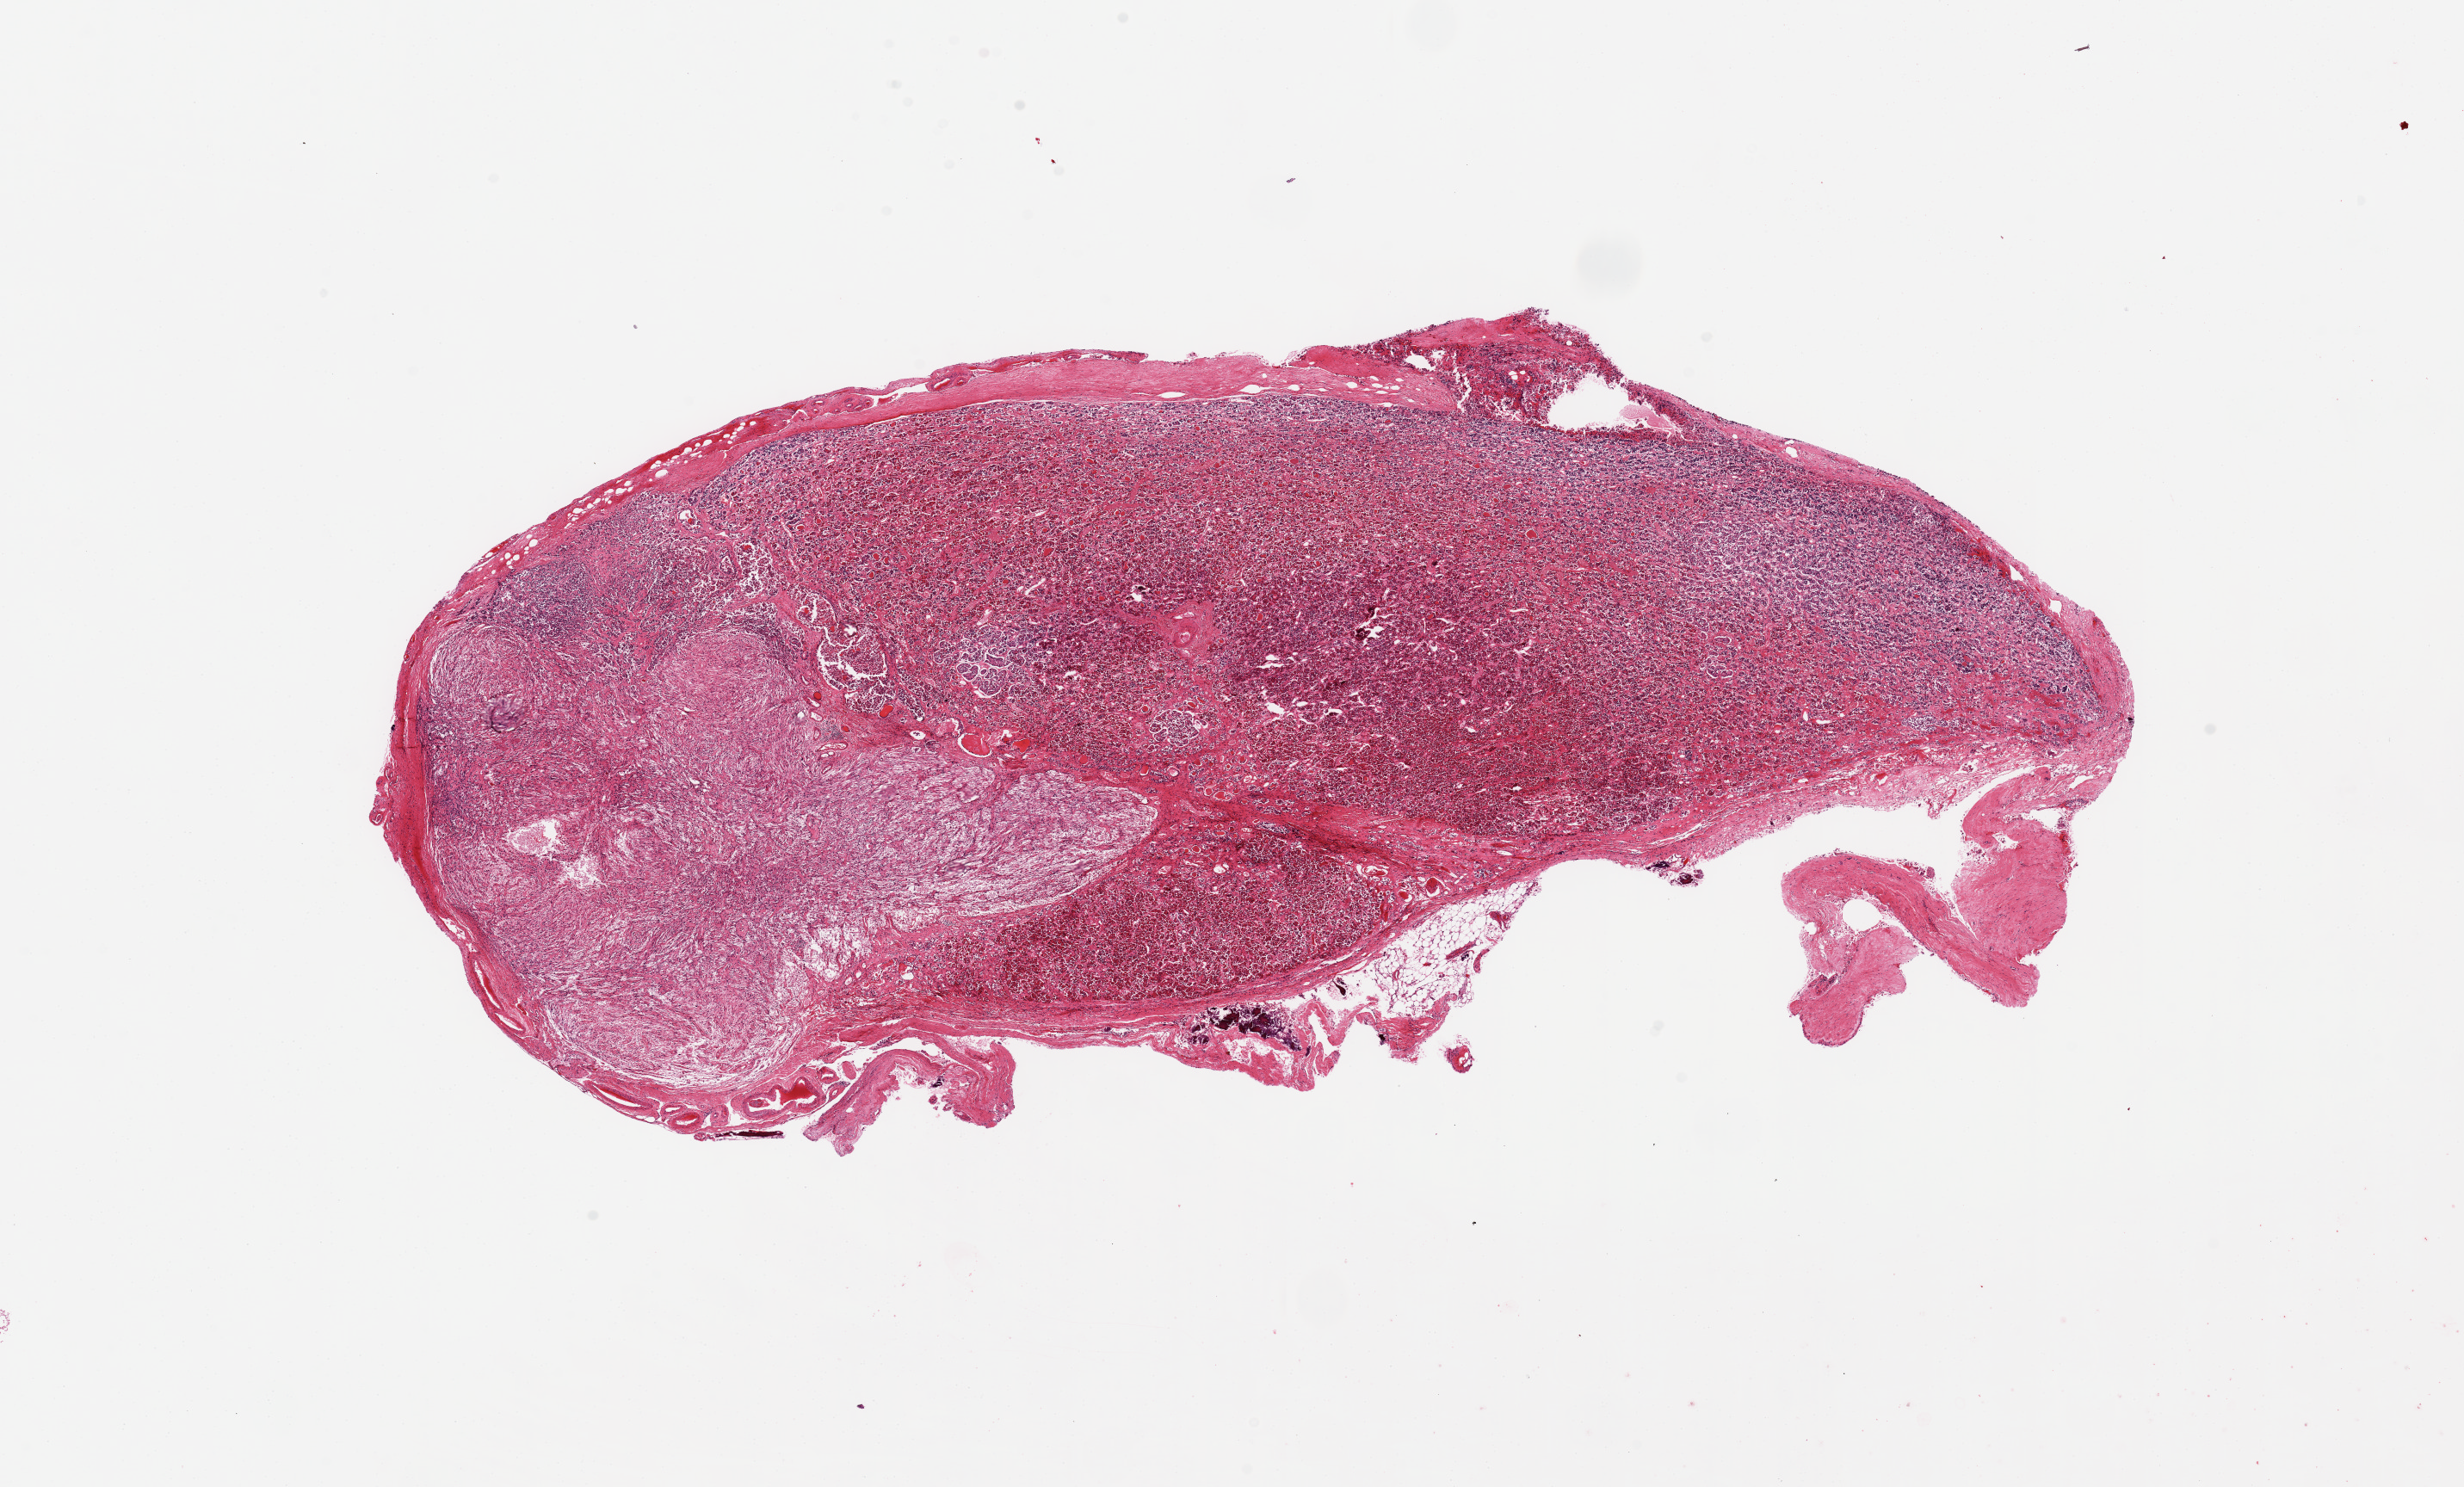
Whole-slide image, haematoxylin and eosin stain — shown as a low-resolution overview of the whole scanned area (about 22.6 x 13.7 mm, acquisition: 20x scan). PAXgene-fixed, paraffin-embedded tissue. Section of pituitary (target tissue). Donor tissue sample. Donor sex: female.
Reviewer comment on this tissue sample: 16x6 mm; anterior and poasterior.